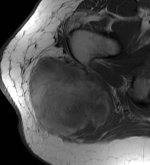
MRI of an extremity soft-tissue mass, one axial slice; slice 31 of 56 in the series (ordered by position); MR volume resampled by the dataset authors to the PET/CT grid (not the native acquisition matrix); 150 × 165 image matrix, field of view 146 × 161 mm. Female patient. Case-level facts recorded for this patient, not image findings: histological type: epithelioid sarcoma with vascular differentiation; site of the primary tumour: right buttock.
Outlined on this slice (expert contour drawn on MRI and transferred to this co-registered scan by the dataset authors):
- gross tumour volume (mass): bounding box [x1, y1, x2, y2] px = [25, 54, 115, 139]